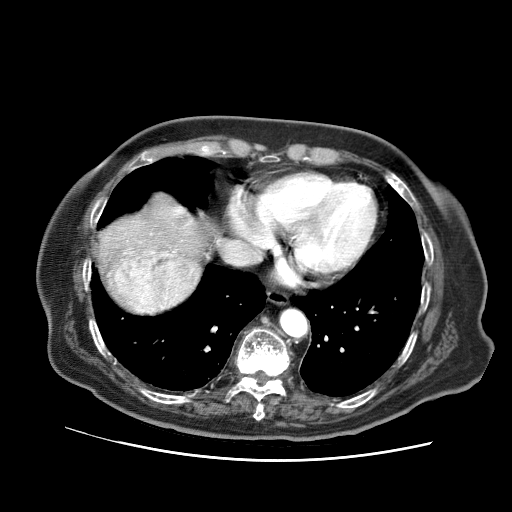
Contrast-enhanced abdominal CT (liver protocol), one axial slice; slice 62 of 73 in the series (ordered by position); reconstruction kernel STANDARD; 120 kVp; soft-tissue window (W 400 / L 40 HU); 512 × 512 image matrix, field of view 380 × 380 mm. From the clinical record (not read from this slice): diagnosis: hepatocellular carcinoma (patient treated with transarterial chemoembolisation; whether this scan precedes or follows treatment is not stated here); TNM stage (as recorded): Stage-I; Child-Pugh class: A.
Outlined on this slice (semi-automatic segmentation, software-assisted and operator-edited):
- abdominal aorta: bounding box (x1, y1, x2, y2) in pixels: (281, 310, 308, 338)
- liver parenchyma outside the tumour (the mass and vessels are separate outlines, so this box may not span the whole liver): (96, 197, 206, 311)
- mass: (112, 253, 200, 314)
- liver vessels: (125, 208, 183, 254)